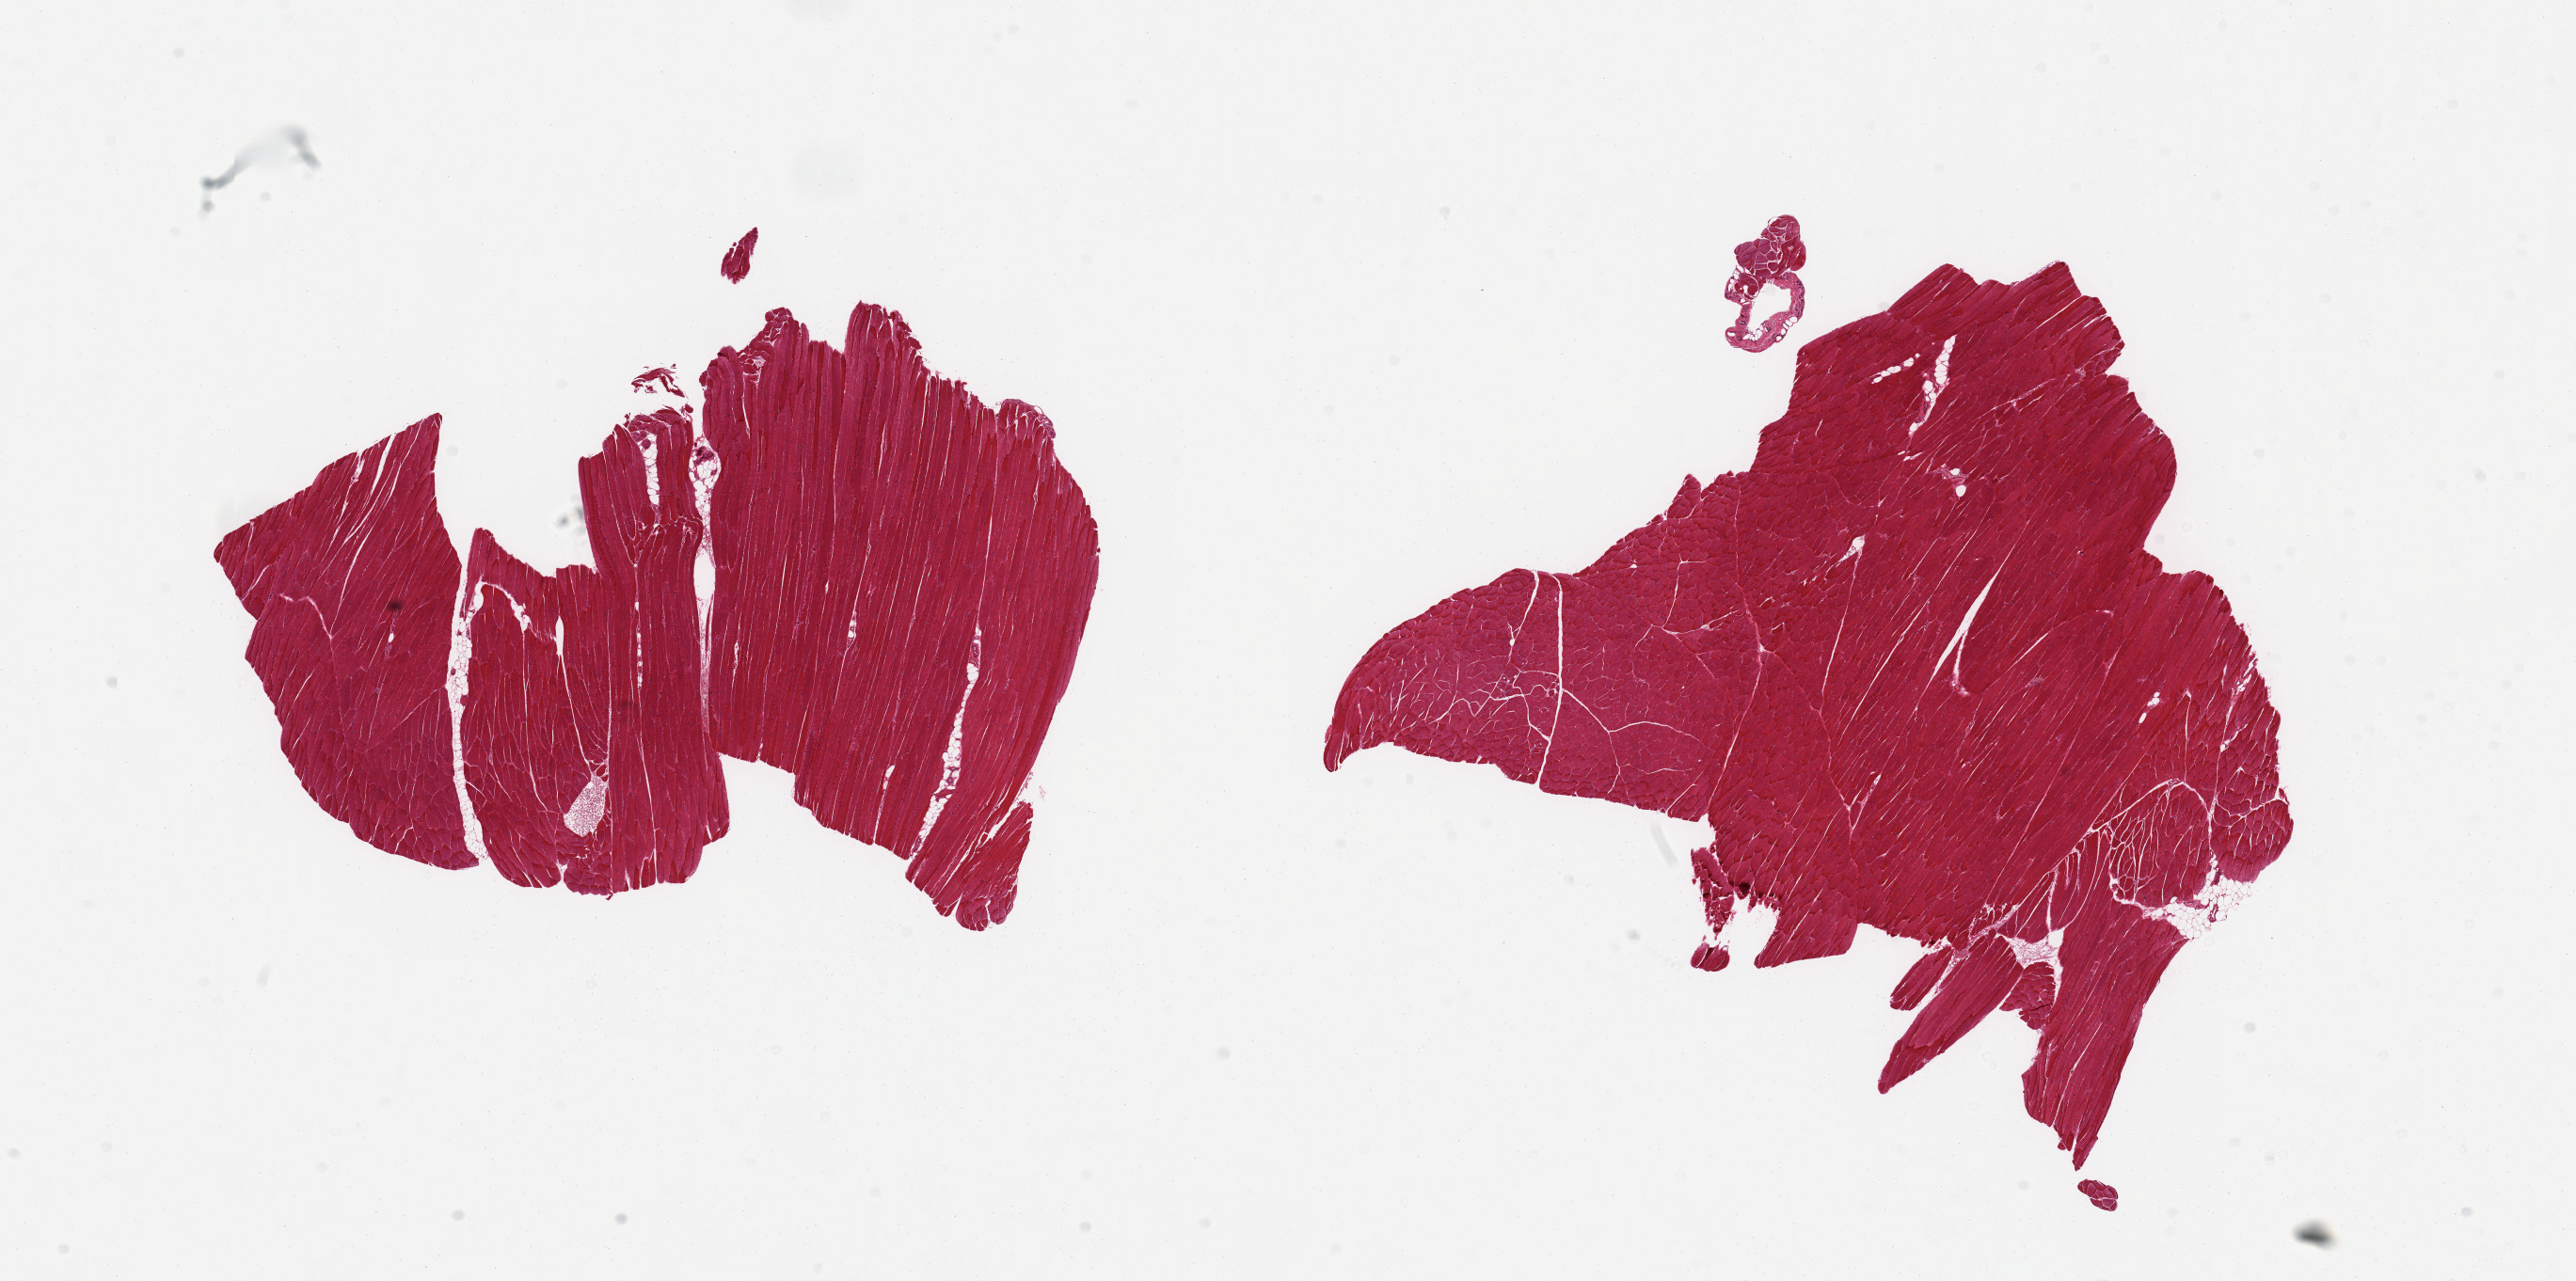
Digitized hematoxylin and eosin (H&E)-stained section, brightfield, whole scanned area (about 21.7 x 10.8 mm, acquisition: 20x scan) shown as a low-resolution overview; PAXgene-fixed paraffin-embedded (PFPE) section; sampled site (target tissue): skeletal muscle; tissue donor sample.
• review note (as recorded): 2 pieces, ~10% interstitial fat